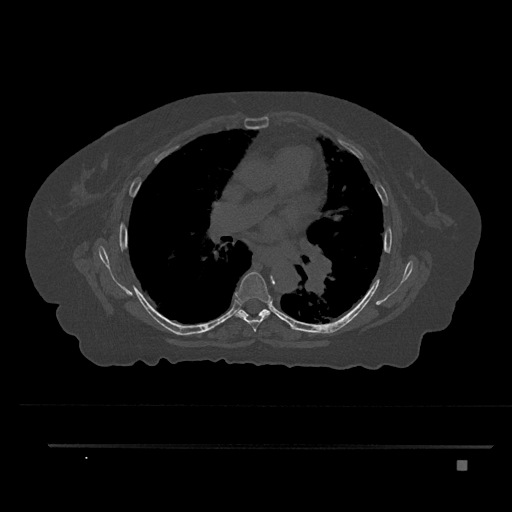
CT including the spine, one axial slice. Slice 514 of 797 in the series (ordered by position). 120 kVp. Bone window (W 1800 / L 400 HU). 0.5 mm slice thickness. 512 × 512 image matrix. Female patient, age 76 years. From the clinical record (not read from this slice): primary cancer: lung.
Outlined on this slice (semi-automatically segmented with operator editing):
- T6 vertebra: bounding box (x1, y1, x2, y2) in pixels: (235, 271, 272, 332)
- T7 vertebra: (238, 309, 270, 317)